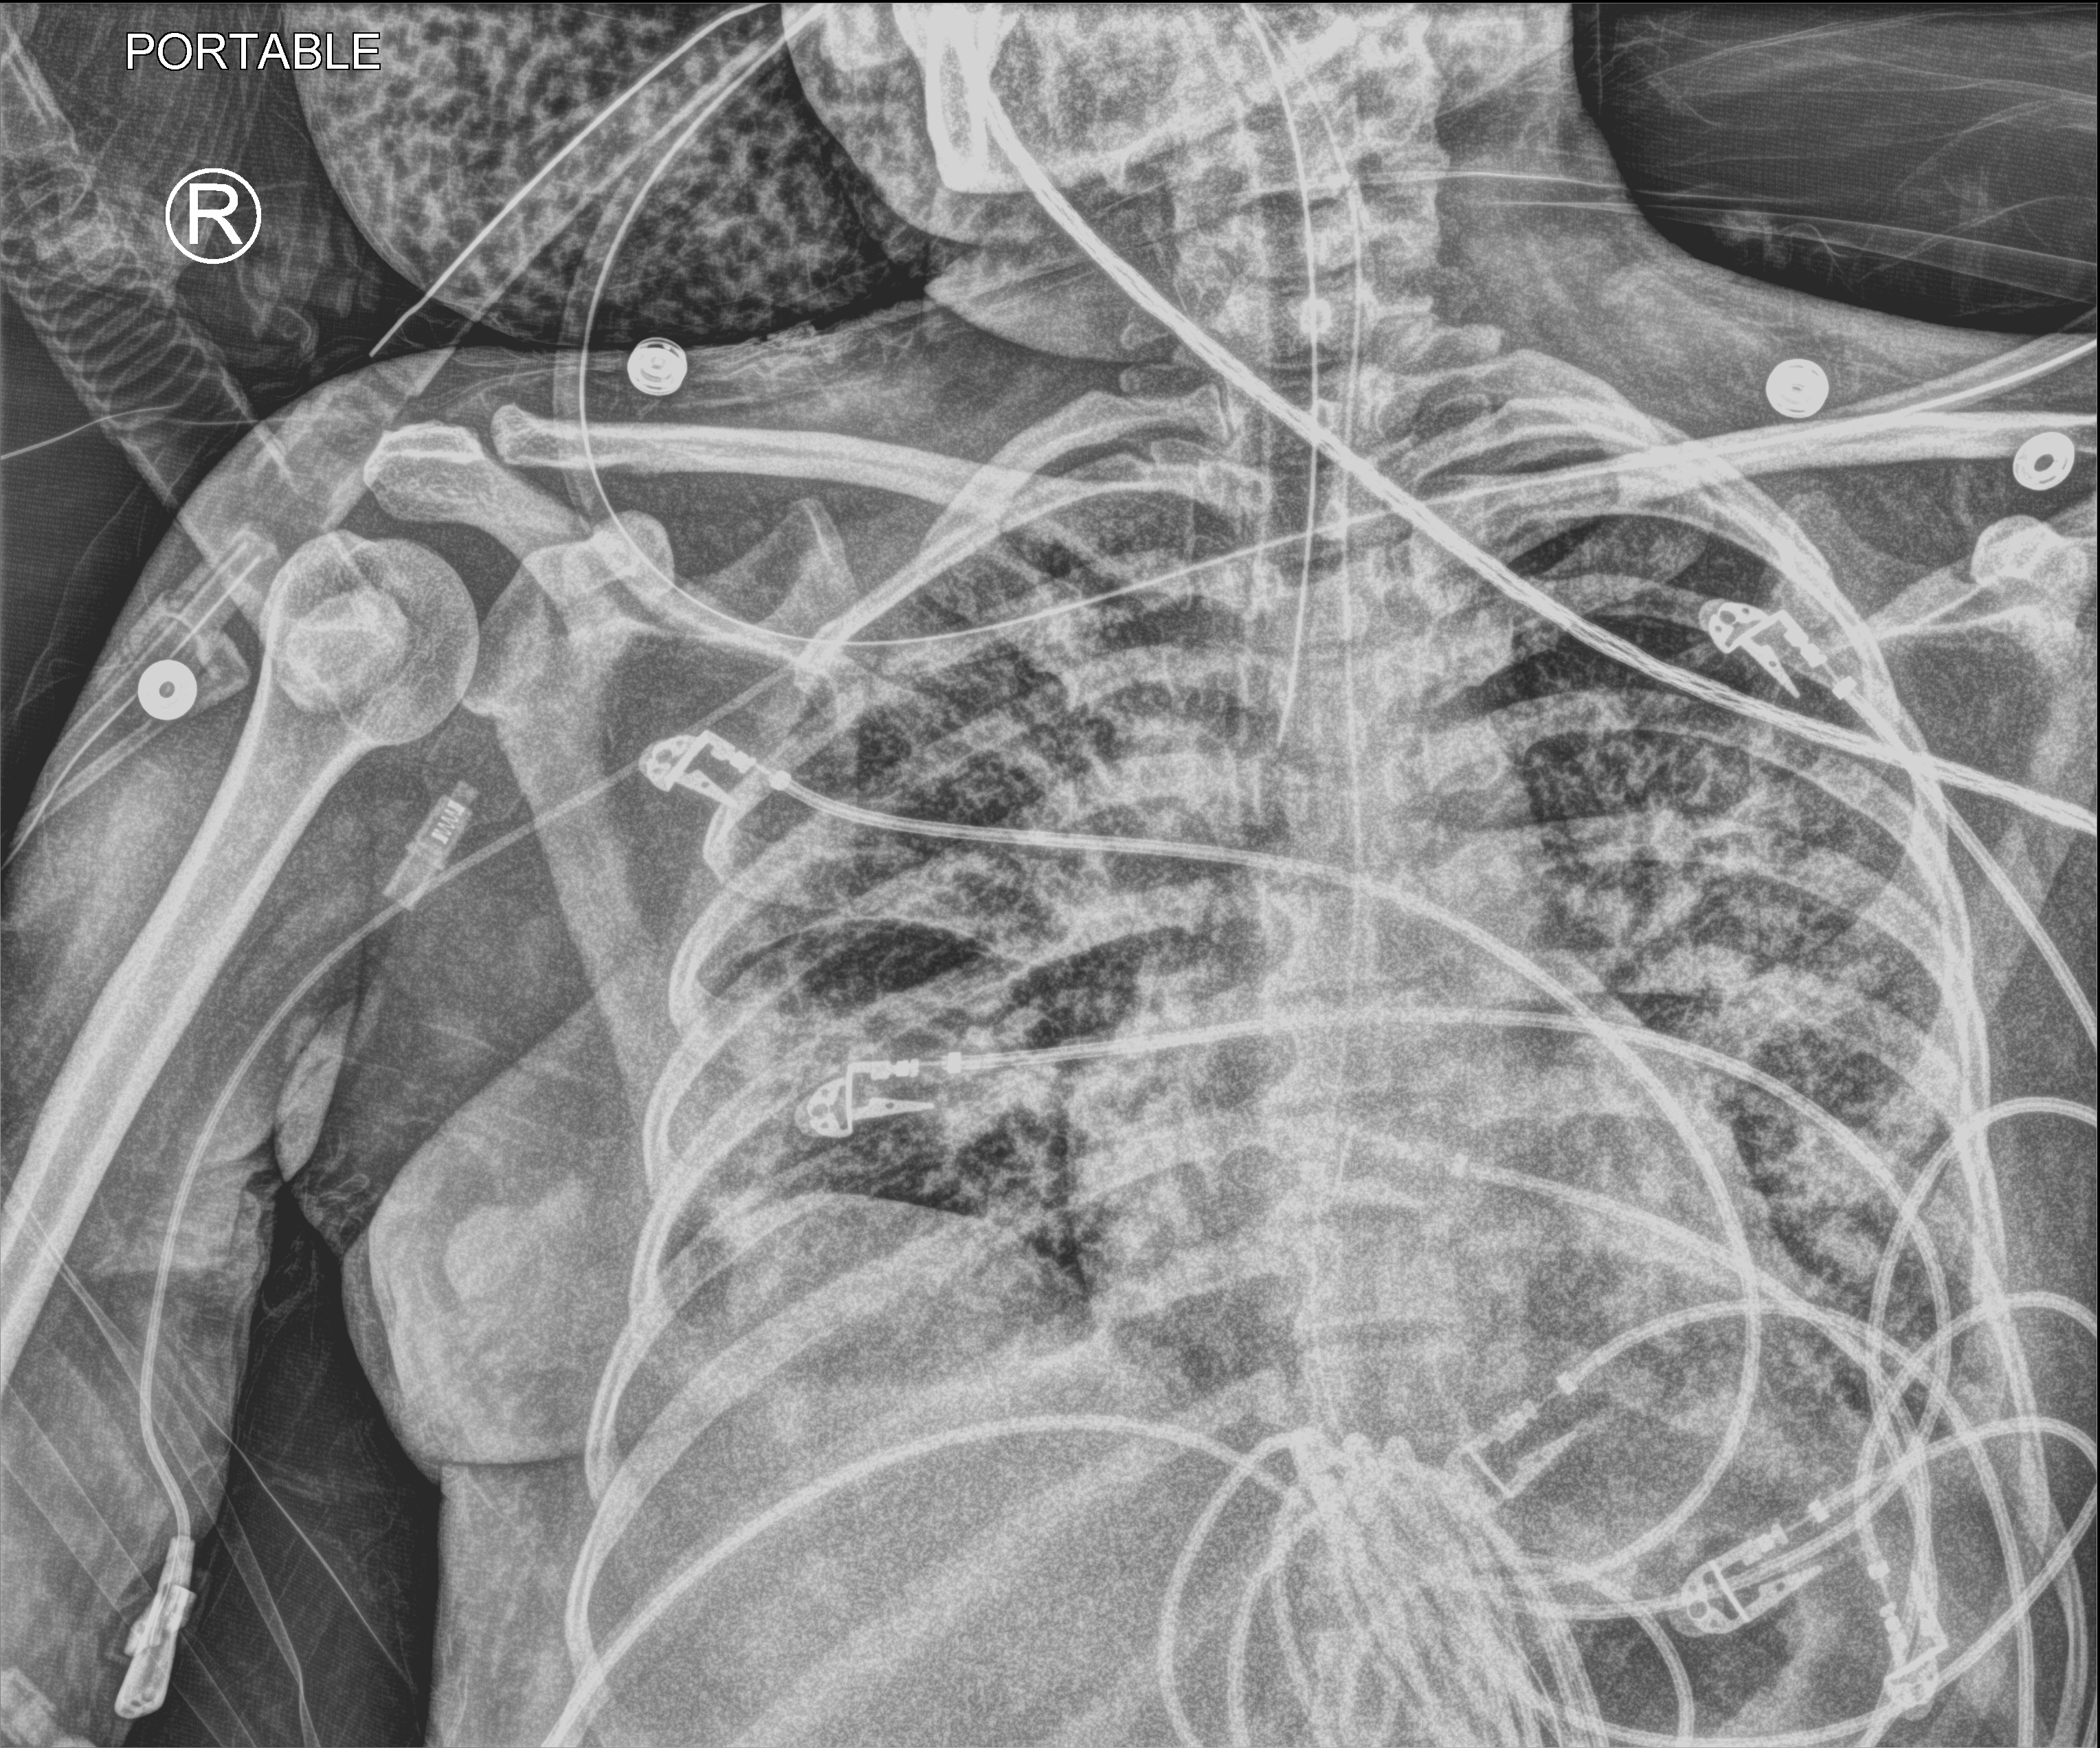
Chest X-ray (portable), anteroposterior (AP) projection. Patient hospitalised with COVID-19; female, aged 18–59 years.
Hospital-stay facts (about this admission, not read from this image; timing relative to this image not recorded): hypertension (admission record): no; mechanically ventilated during this hospital stay: yes; chronic kidney disease (admission record): no.